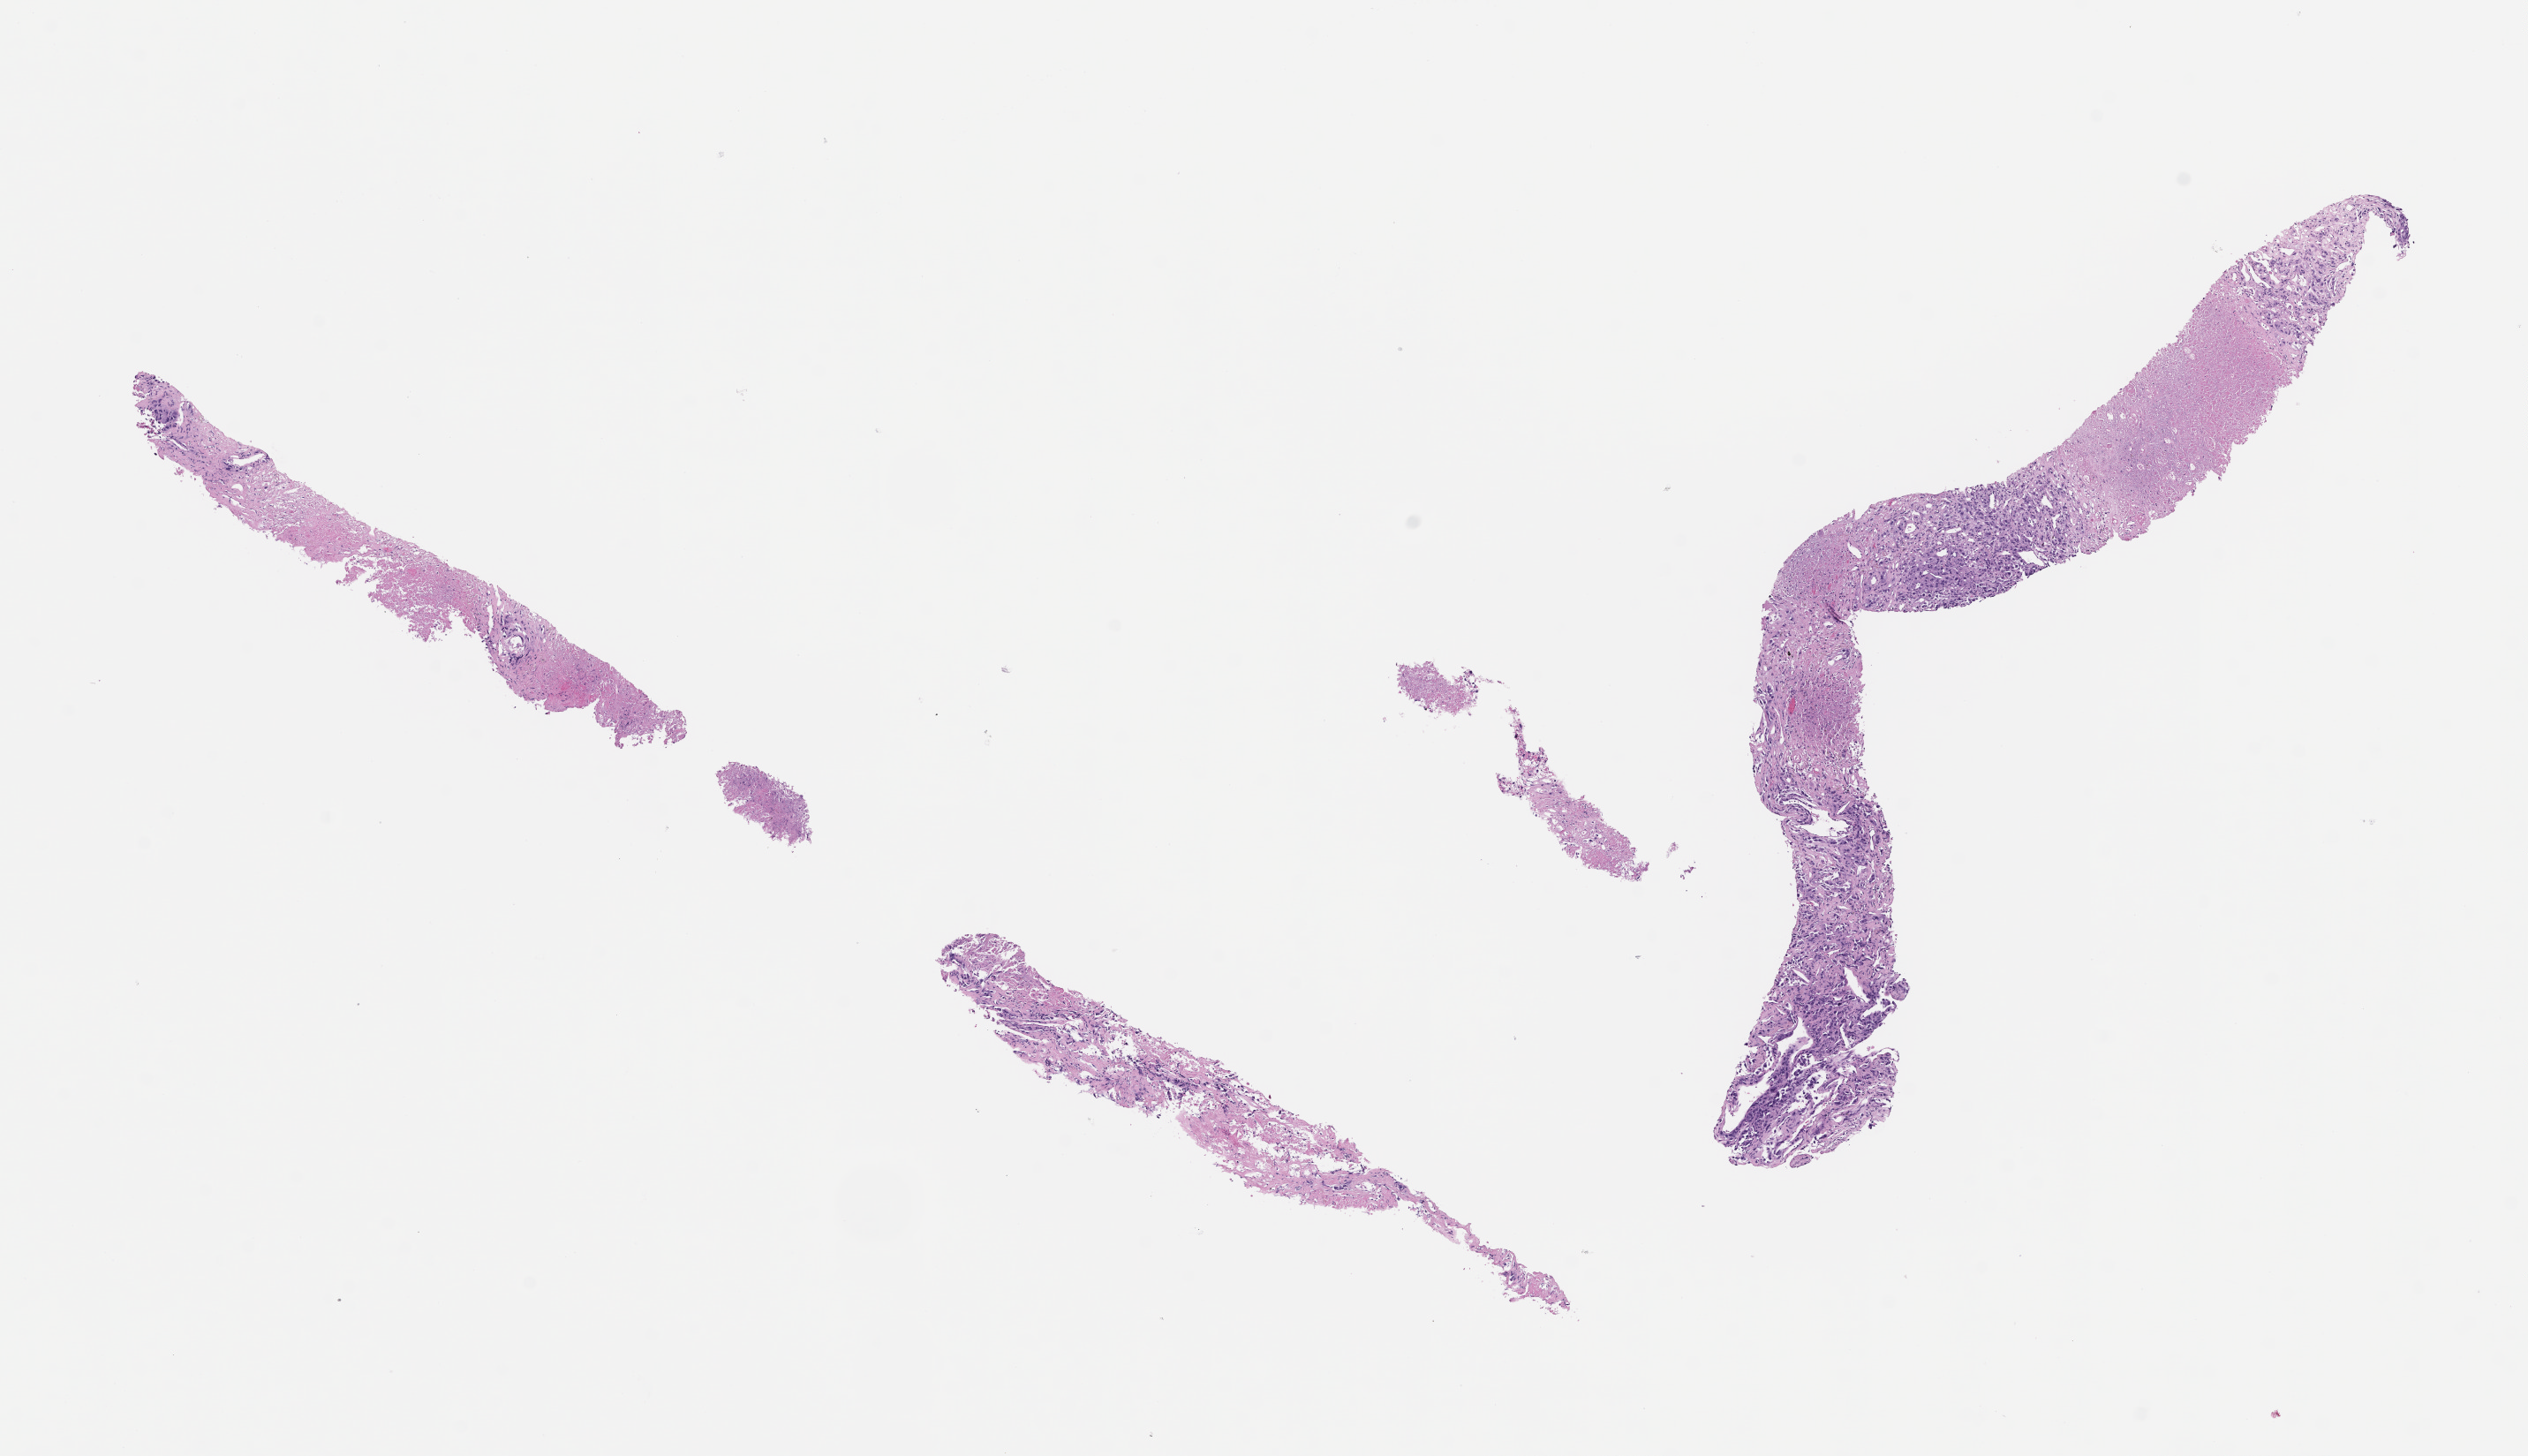
Whole-slide image, H&E stain — a low-resolution overview of the entire scanned area, about 11.6 x 6.7 mm; formalin-fixed paraffin-embedded section; site: lung. Patient: female.
• this section: primary tumour tissue
• diagnosis: Non-Small Cell Lung Carcinoma